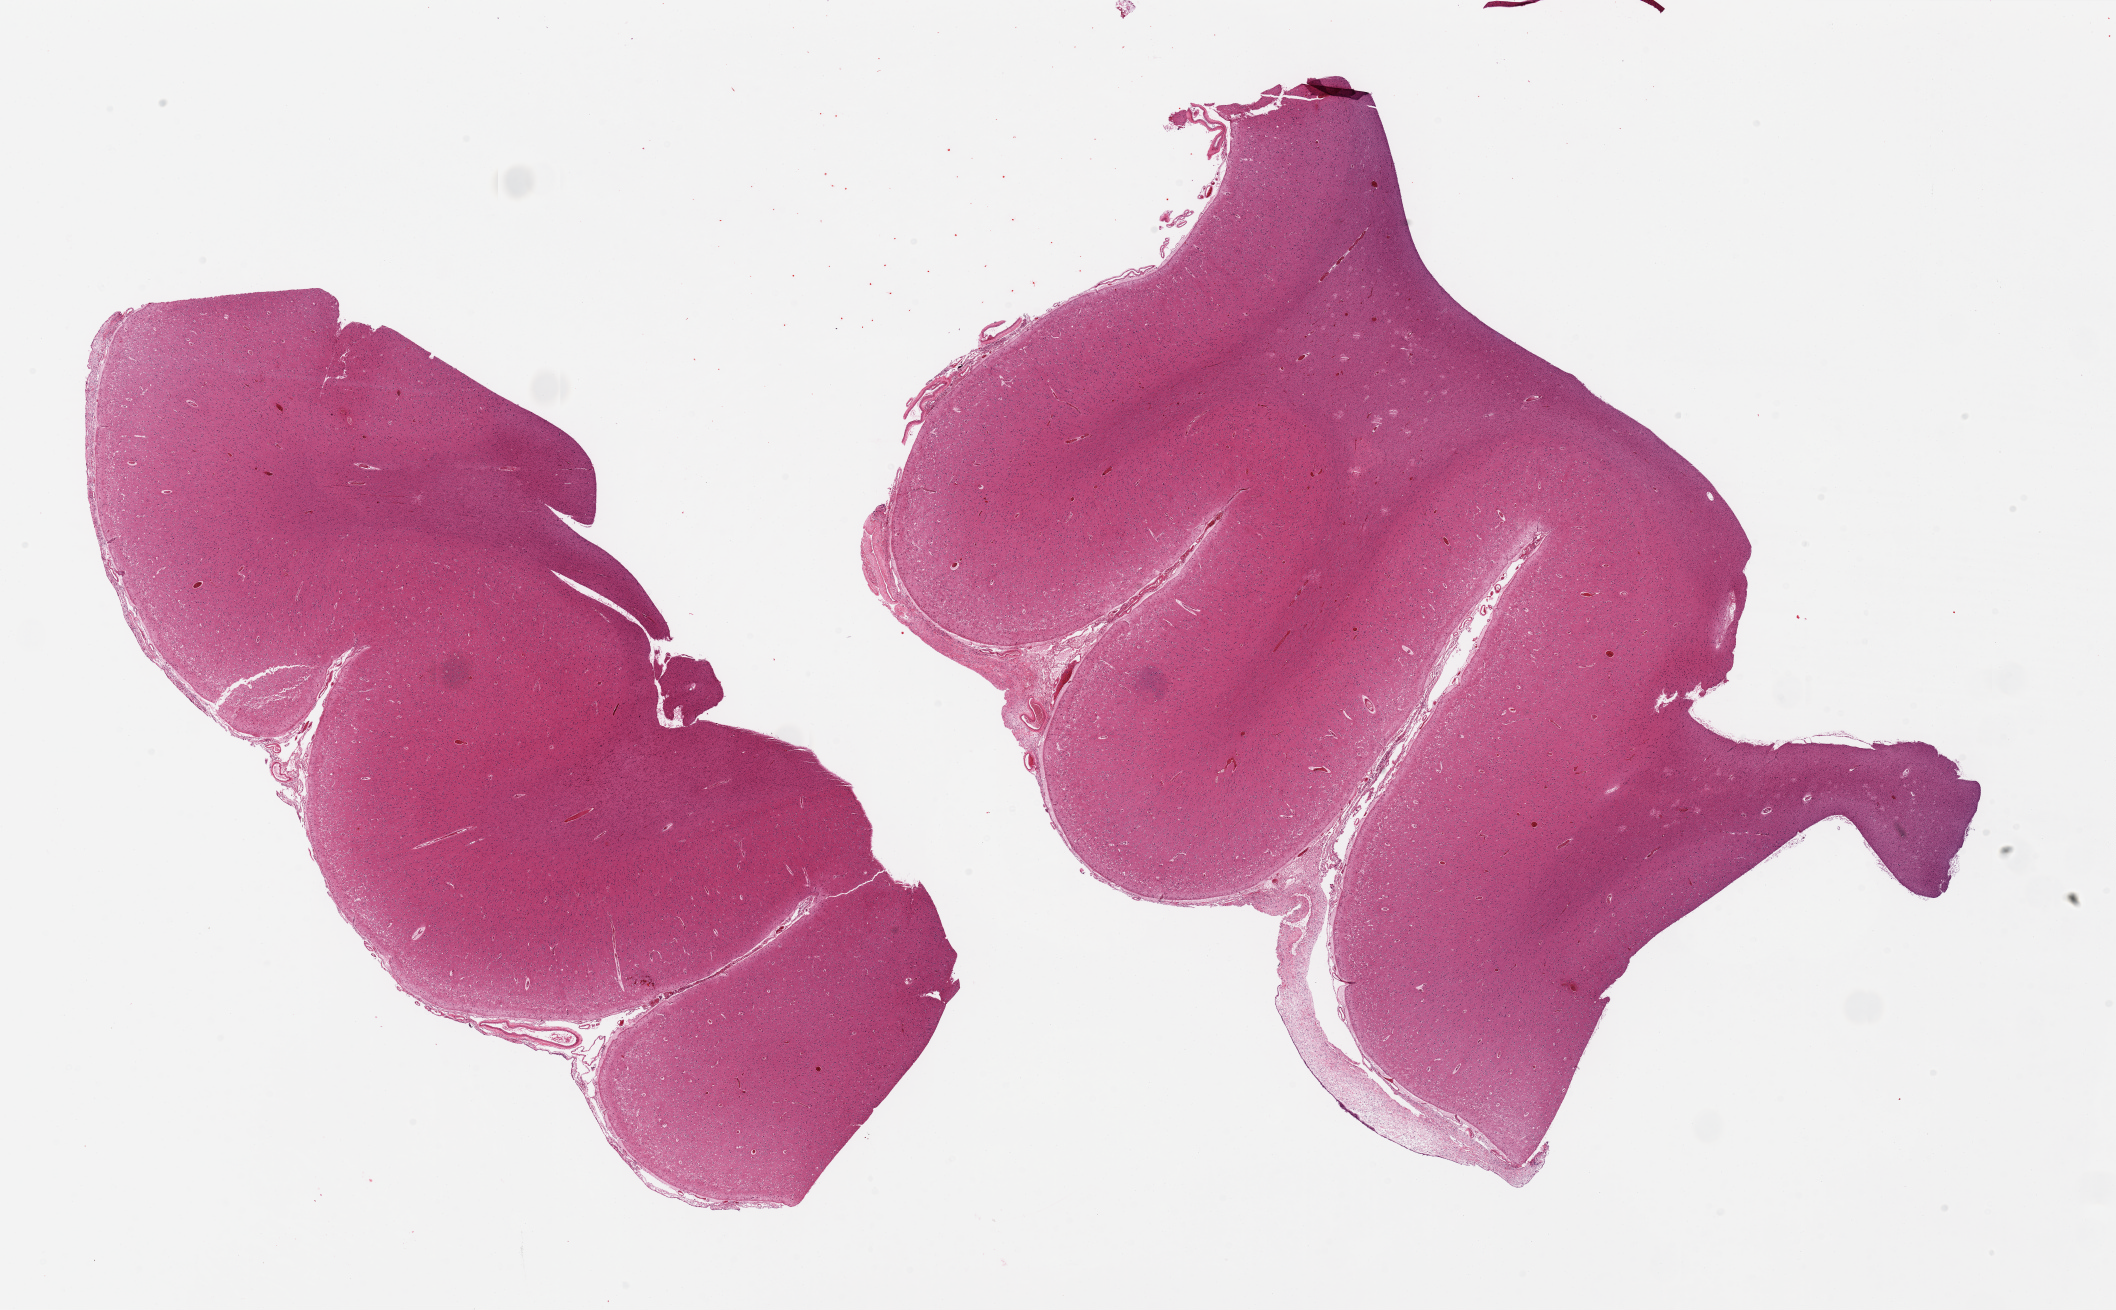
Digitized hematoxylin and eosin (H&E)-stained section, brightfield — whole scanned area (about 33.5 x 20.7 mm) shown as a low-resolution overview. PAXgene-fixed, paraffin-embedded tissue. Sampled site (target tissue): cerebral cortex. Donor tissue sample. Donor sex: male.
- pathologist's review note for this sample: 2 pieces, 1 with meninges (up to 0.77mm thick)